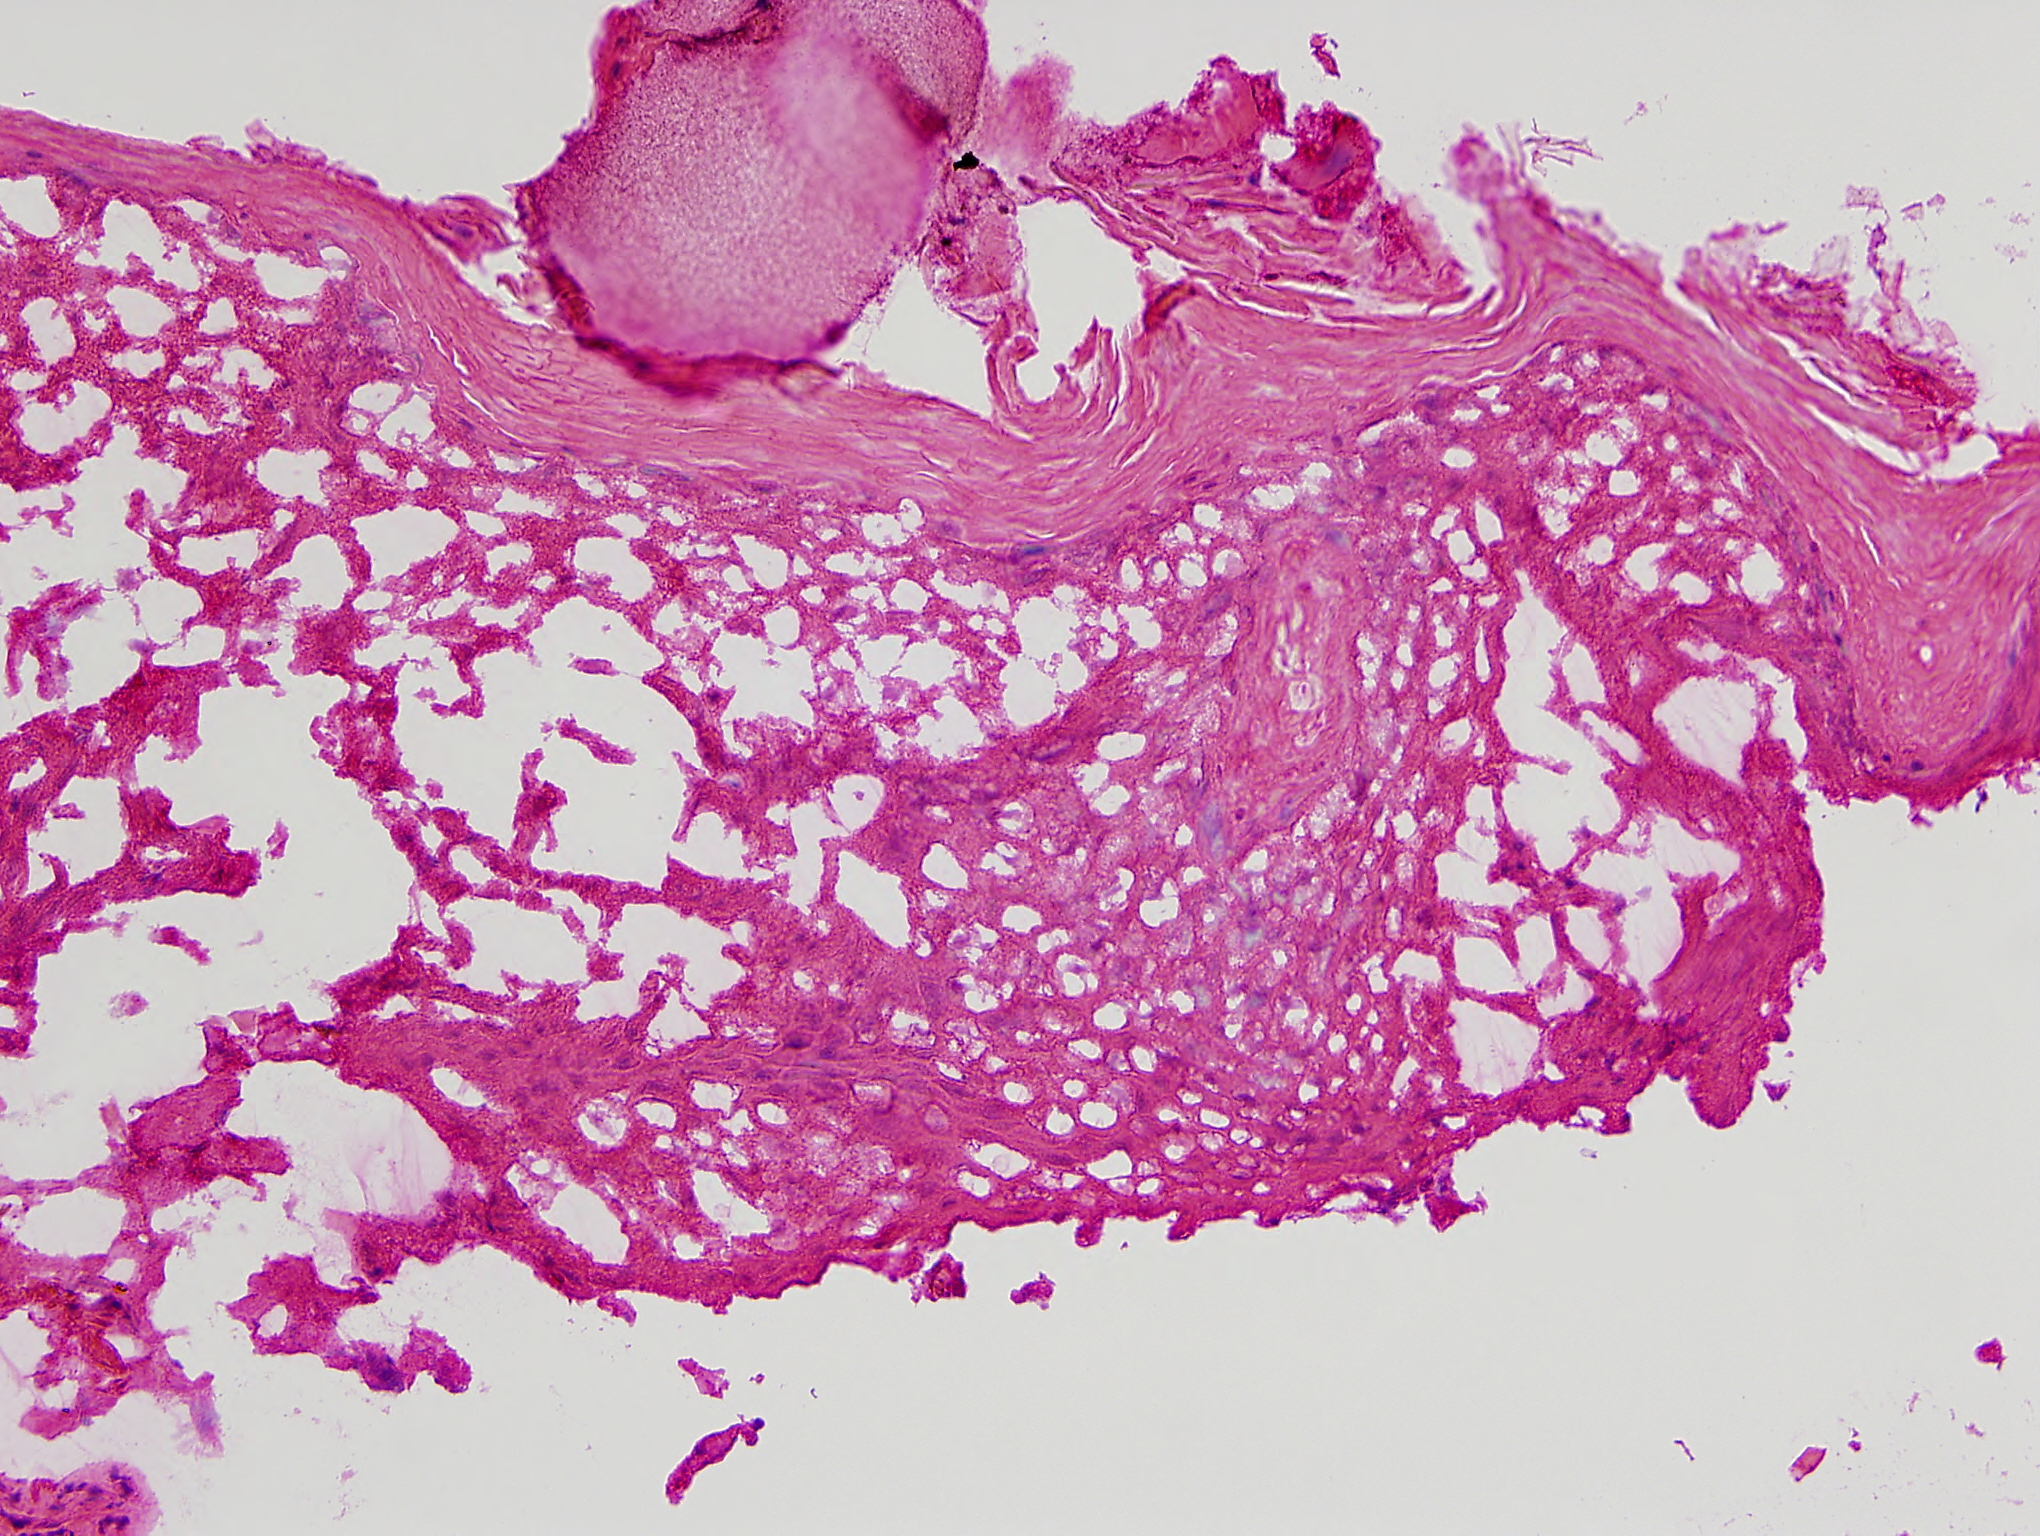
H&E micrograph of a single small tissue field, covering about 1.0 x 0.8 mm, frozen section from the top of the tissue portion, head and neck, solid tissue normal (non-tumour tissue) sample. Patient: female, age at initial diagnosis 77 years.
This section: solid tissue normal (non-tumour) sample from the same patient. Patient diagnosis: Squamous cell carcinoma, NOS (overlapping lesion of lip, oral cavity and pharynx).